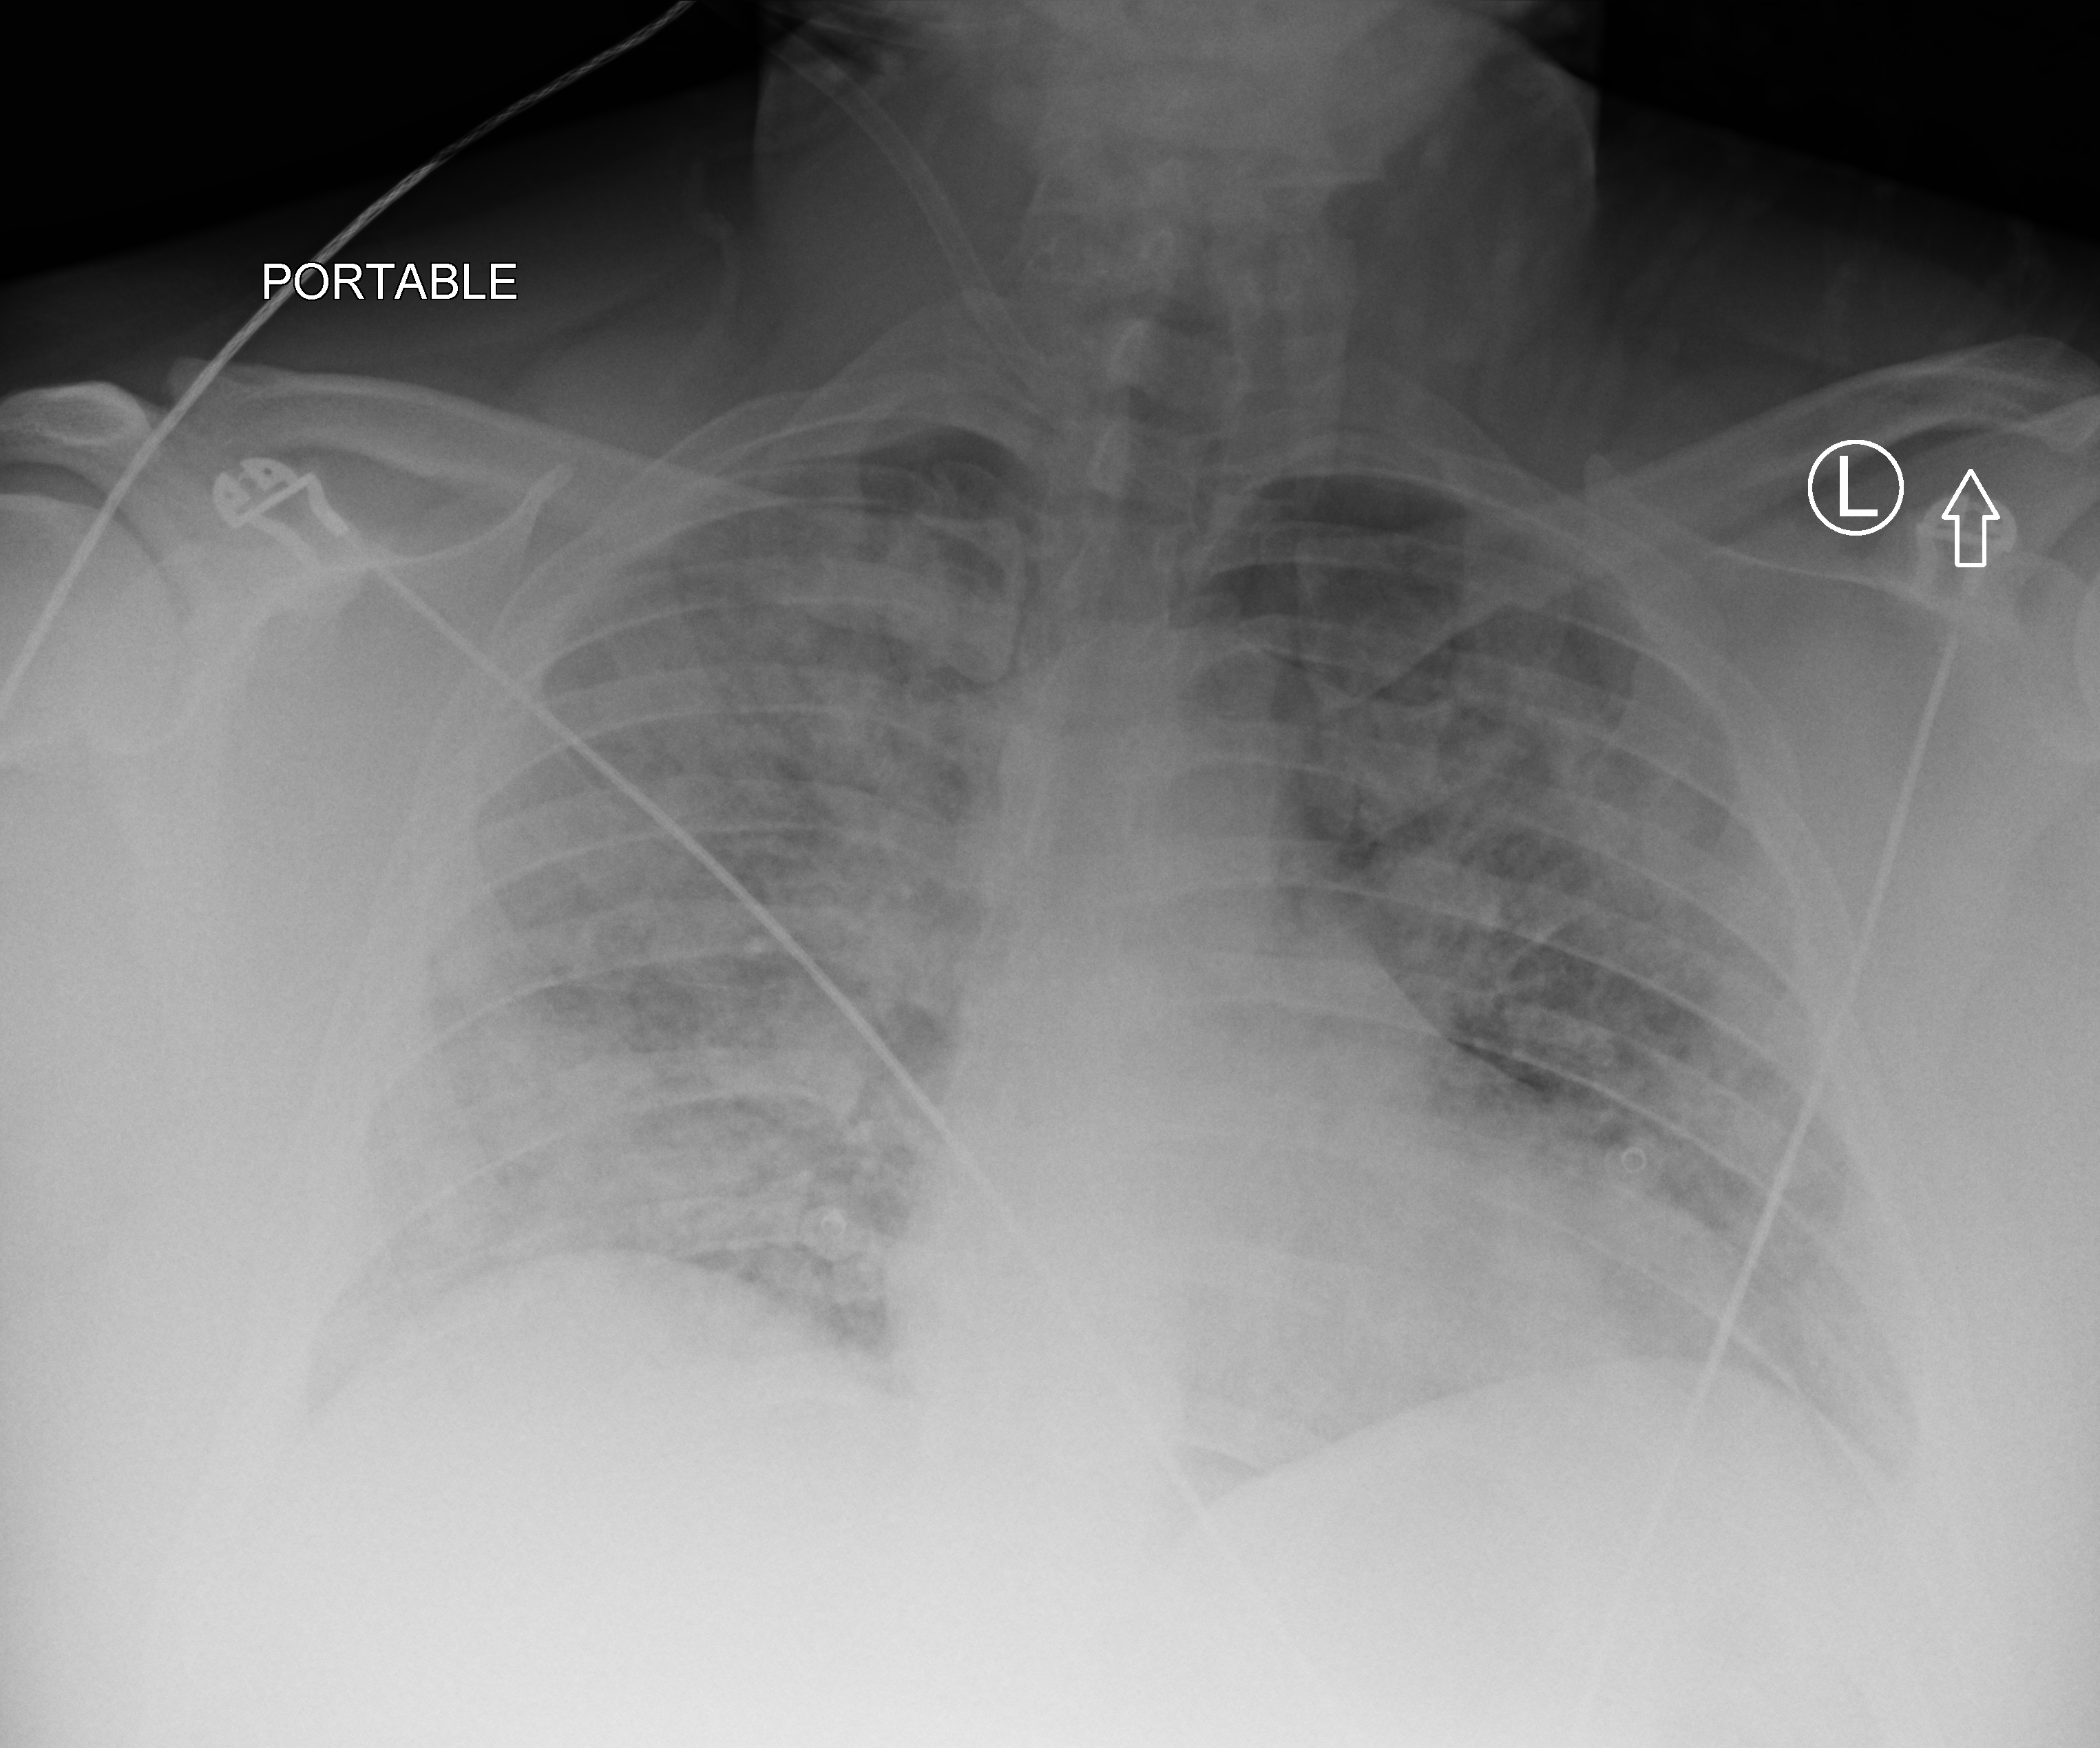
Bedside chest radiograph (computed radiography); anteroposterior (AP) projection. Male patient hospitalised with COVID-19, age 18–59 years.
From the hospital-stay record, not from the radiograph (when in the stay this image was taken is not recorded):
- mechanically ventilated during this hospital stay: no
- hypertension (admission record): no